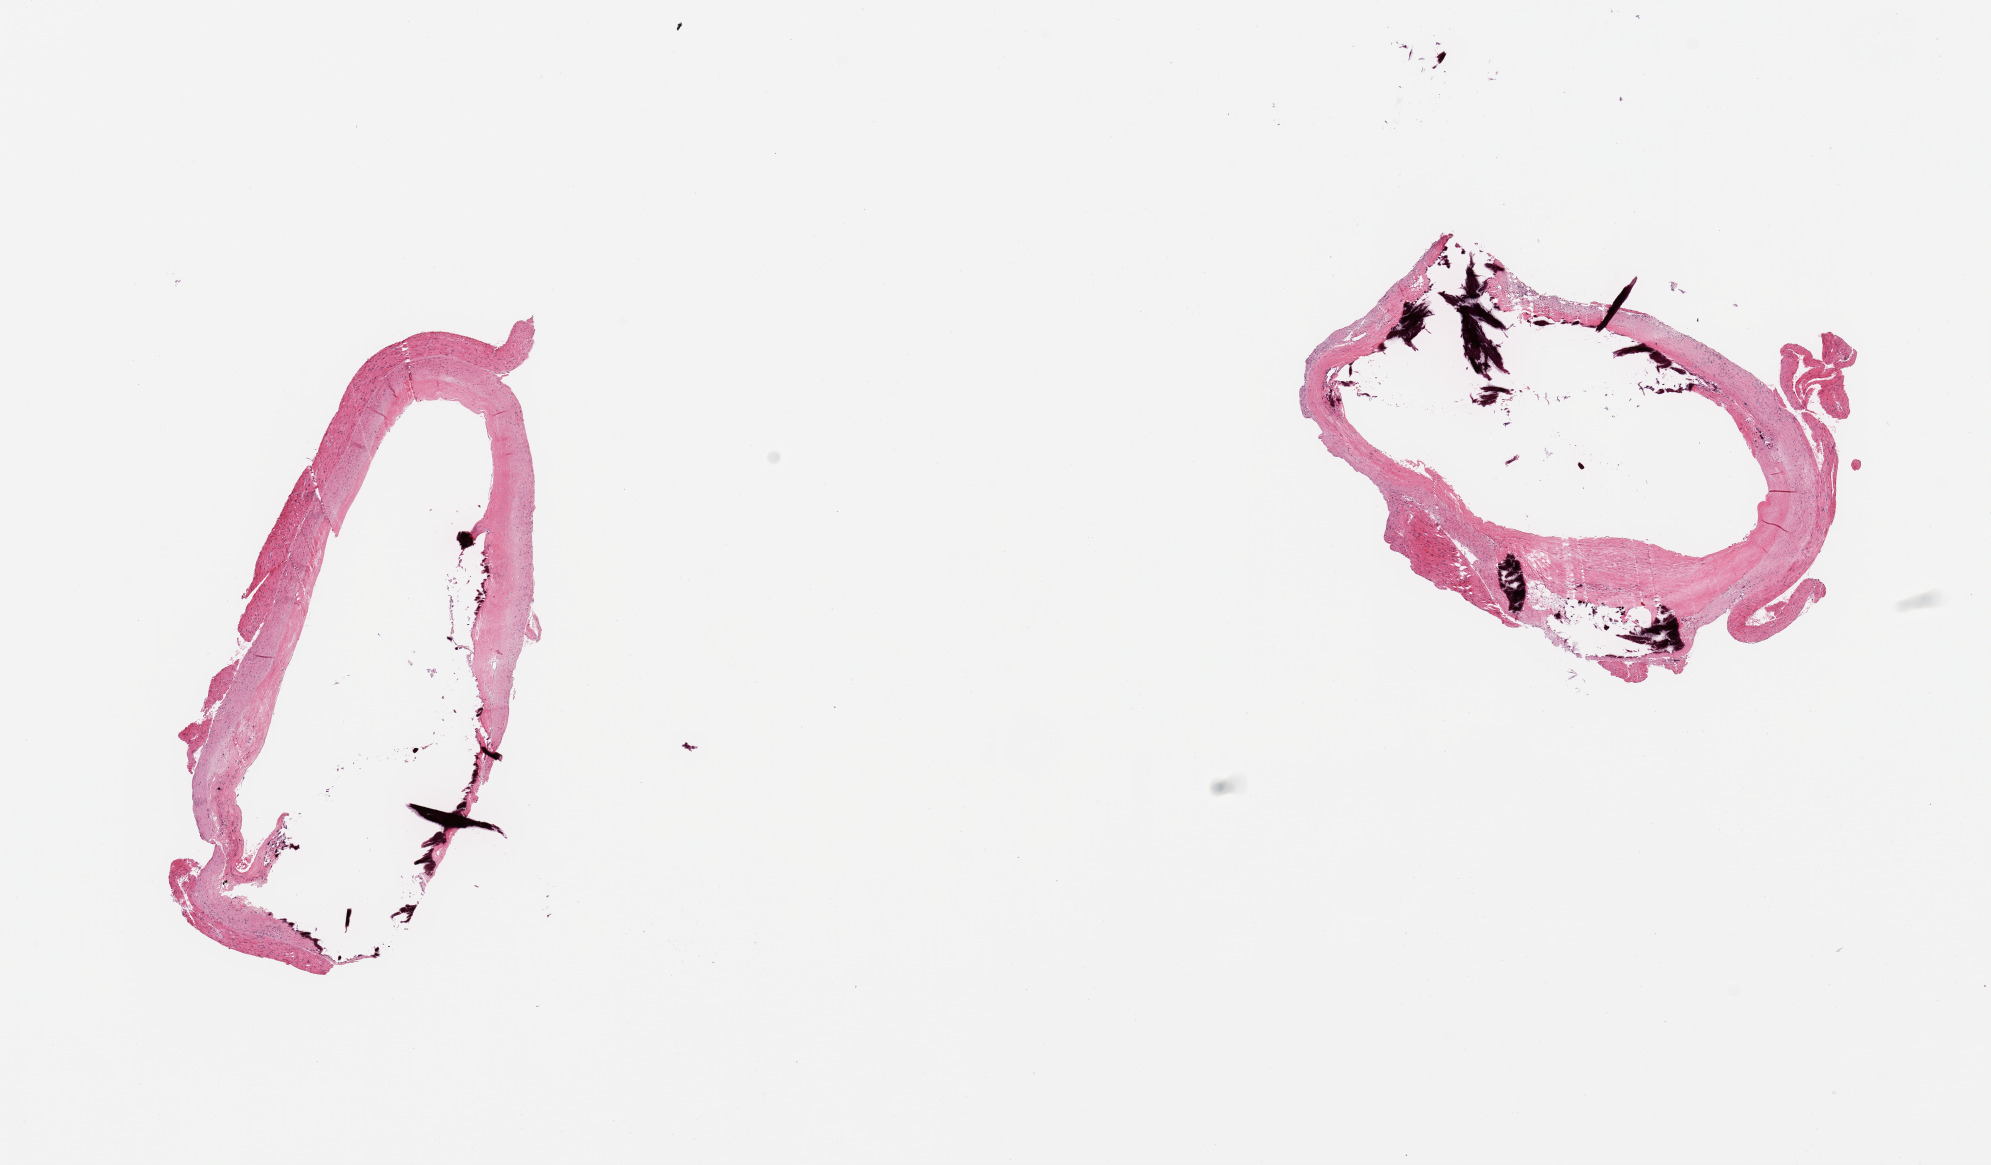
Hematoxylin and eosin (H&E) whole-slide image, brightfield, shown as a low-resolution overview of the whole scanned area (about 15.8 x 9.2 mm, acquisition: 20x scan); PAXgene-fixed, paraffin-embedded tissue; section of coronary artery (target tissue); tissue donor sample. Donor sex: female.
Reviewer comment on this tissue sample: 2 pieces; fragmented, calcific atherosclerosis.